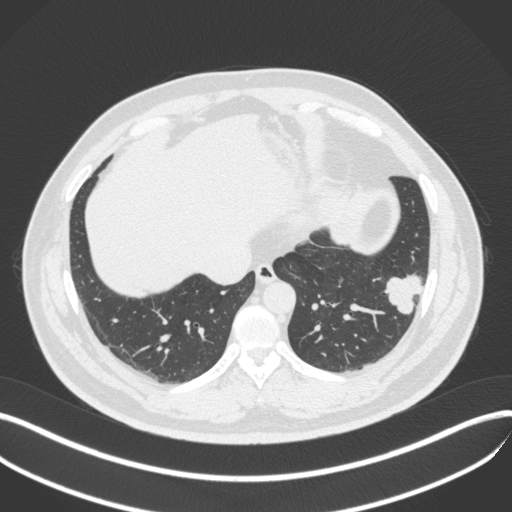
Chest CT, one axial slice. Slice 122 of 420 in the series (ordered by position). Reconstruction kernel B31f. Lung window (W 1500 / L -600 HU). 1 mm slice thickness. 512 × 512 image matrix, field of view 400 × 400 mm. Patient: male, 39 years. From the clinical record (not read from this slice): clinical TNM (as recorded): T2a N0 M0.
Outlined on this slice (rectangle marked by the reading radiologist):
- lung tumour (recorded histology: adenocarcinoma): bounding box [x1, y1, x2, y2] px = [379, 268, 430, 320]